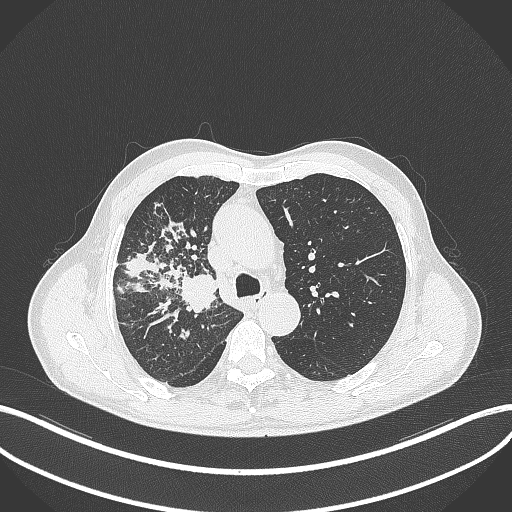
Chest CT, one axial slice. Slice 337 of 490 in the series (ordered by position). Lung window (W 1500 / L -600 HU). 1 mm slice thickness. 512 × 512 image matrix, field of view 400 × 400 mm. Male patient, age 69 years. From the clinical record (not read from this slice): clinical TNM (as recorded): T2a N0 M0.
Structures marked on this image (rectangle marked by the reading radiologist):
- lung tumour (recorded histology: adenocarcinoma): box from (x=178, y=271) to (x=219, y=315) px